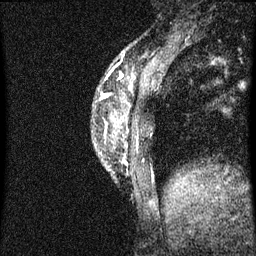
Breast MRI (dynamic contrast-enhanced), one sagittal slice; position 14 of 60 along the scan axis; dynamic contrast-enhanced series, image 2 of 3 at this slice position (ordered by acquisition); 1.5 T; TE 4.2 ms, TR 8 ms; 2 mm slice thickness; 256 × 256 image matrix, field of view 180 × 180 mm. Patient: female, 33 years.
Structures marked on this image (semi-automatically segmented with operator editing):
- analysis volume of interest (the breast-tissue region the enhancement analysis was run in; not a lesion): bounding box [x1, y1, x2, y2] px = [93, 74, 151, 183]
- tumour enhancement mask (voxels above the 70 % enhancement threshold inside the analysis volume of interest): [104, 74, 122, 97]